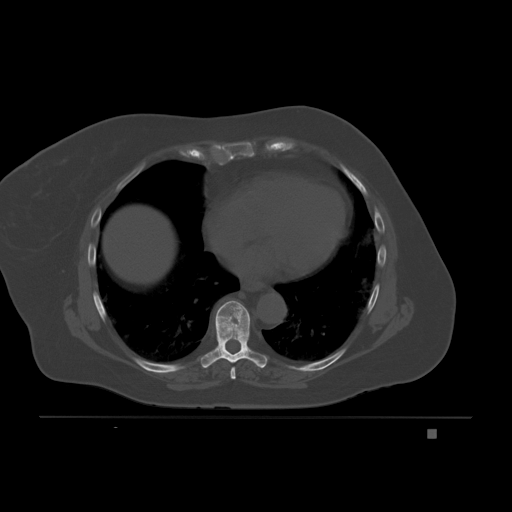
CT including the spine, one axial slice; slice 119 of 221 in the series (ordered by position); bone window (W 1800 / L 400 HU); 3 mm slice thickness; 512 × 512 image matrix, field of view 474 × 474 mm. Patient: female, 63 years. Case-level facts recorded for this patient, not image findings: primary cancer: breast.
Annotated regions visible in this slice (semi-automatic segmentation, software-assisted and operator-edited):
- T7 vertebra: bounding box [x1, y1, x2, y2] px = [230, 367, 236, 380]
- T8 vertebra: [200, 300, 268, 368]